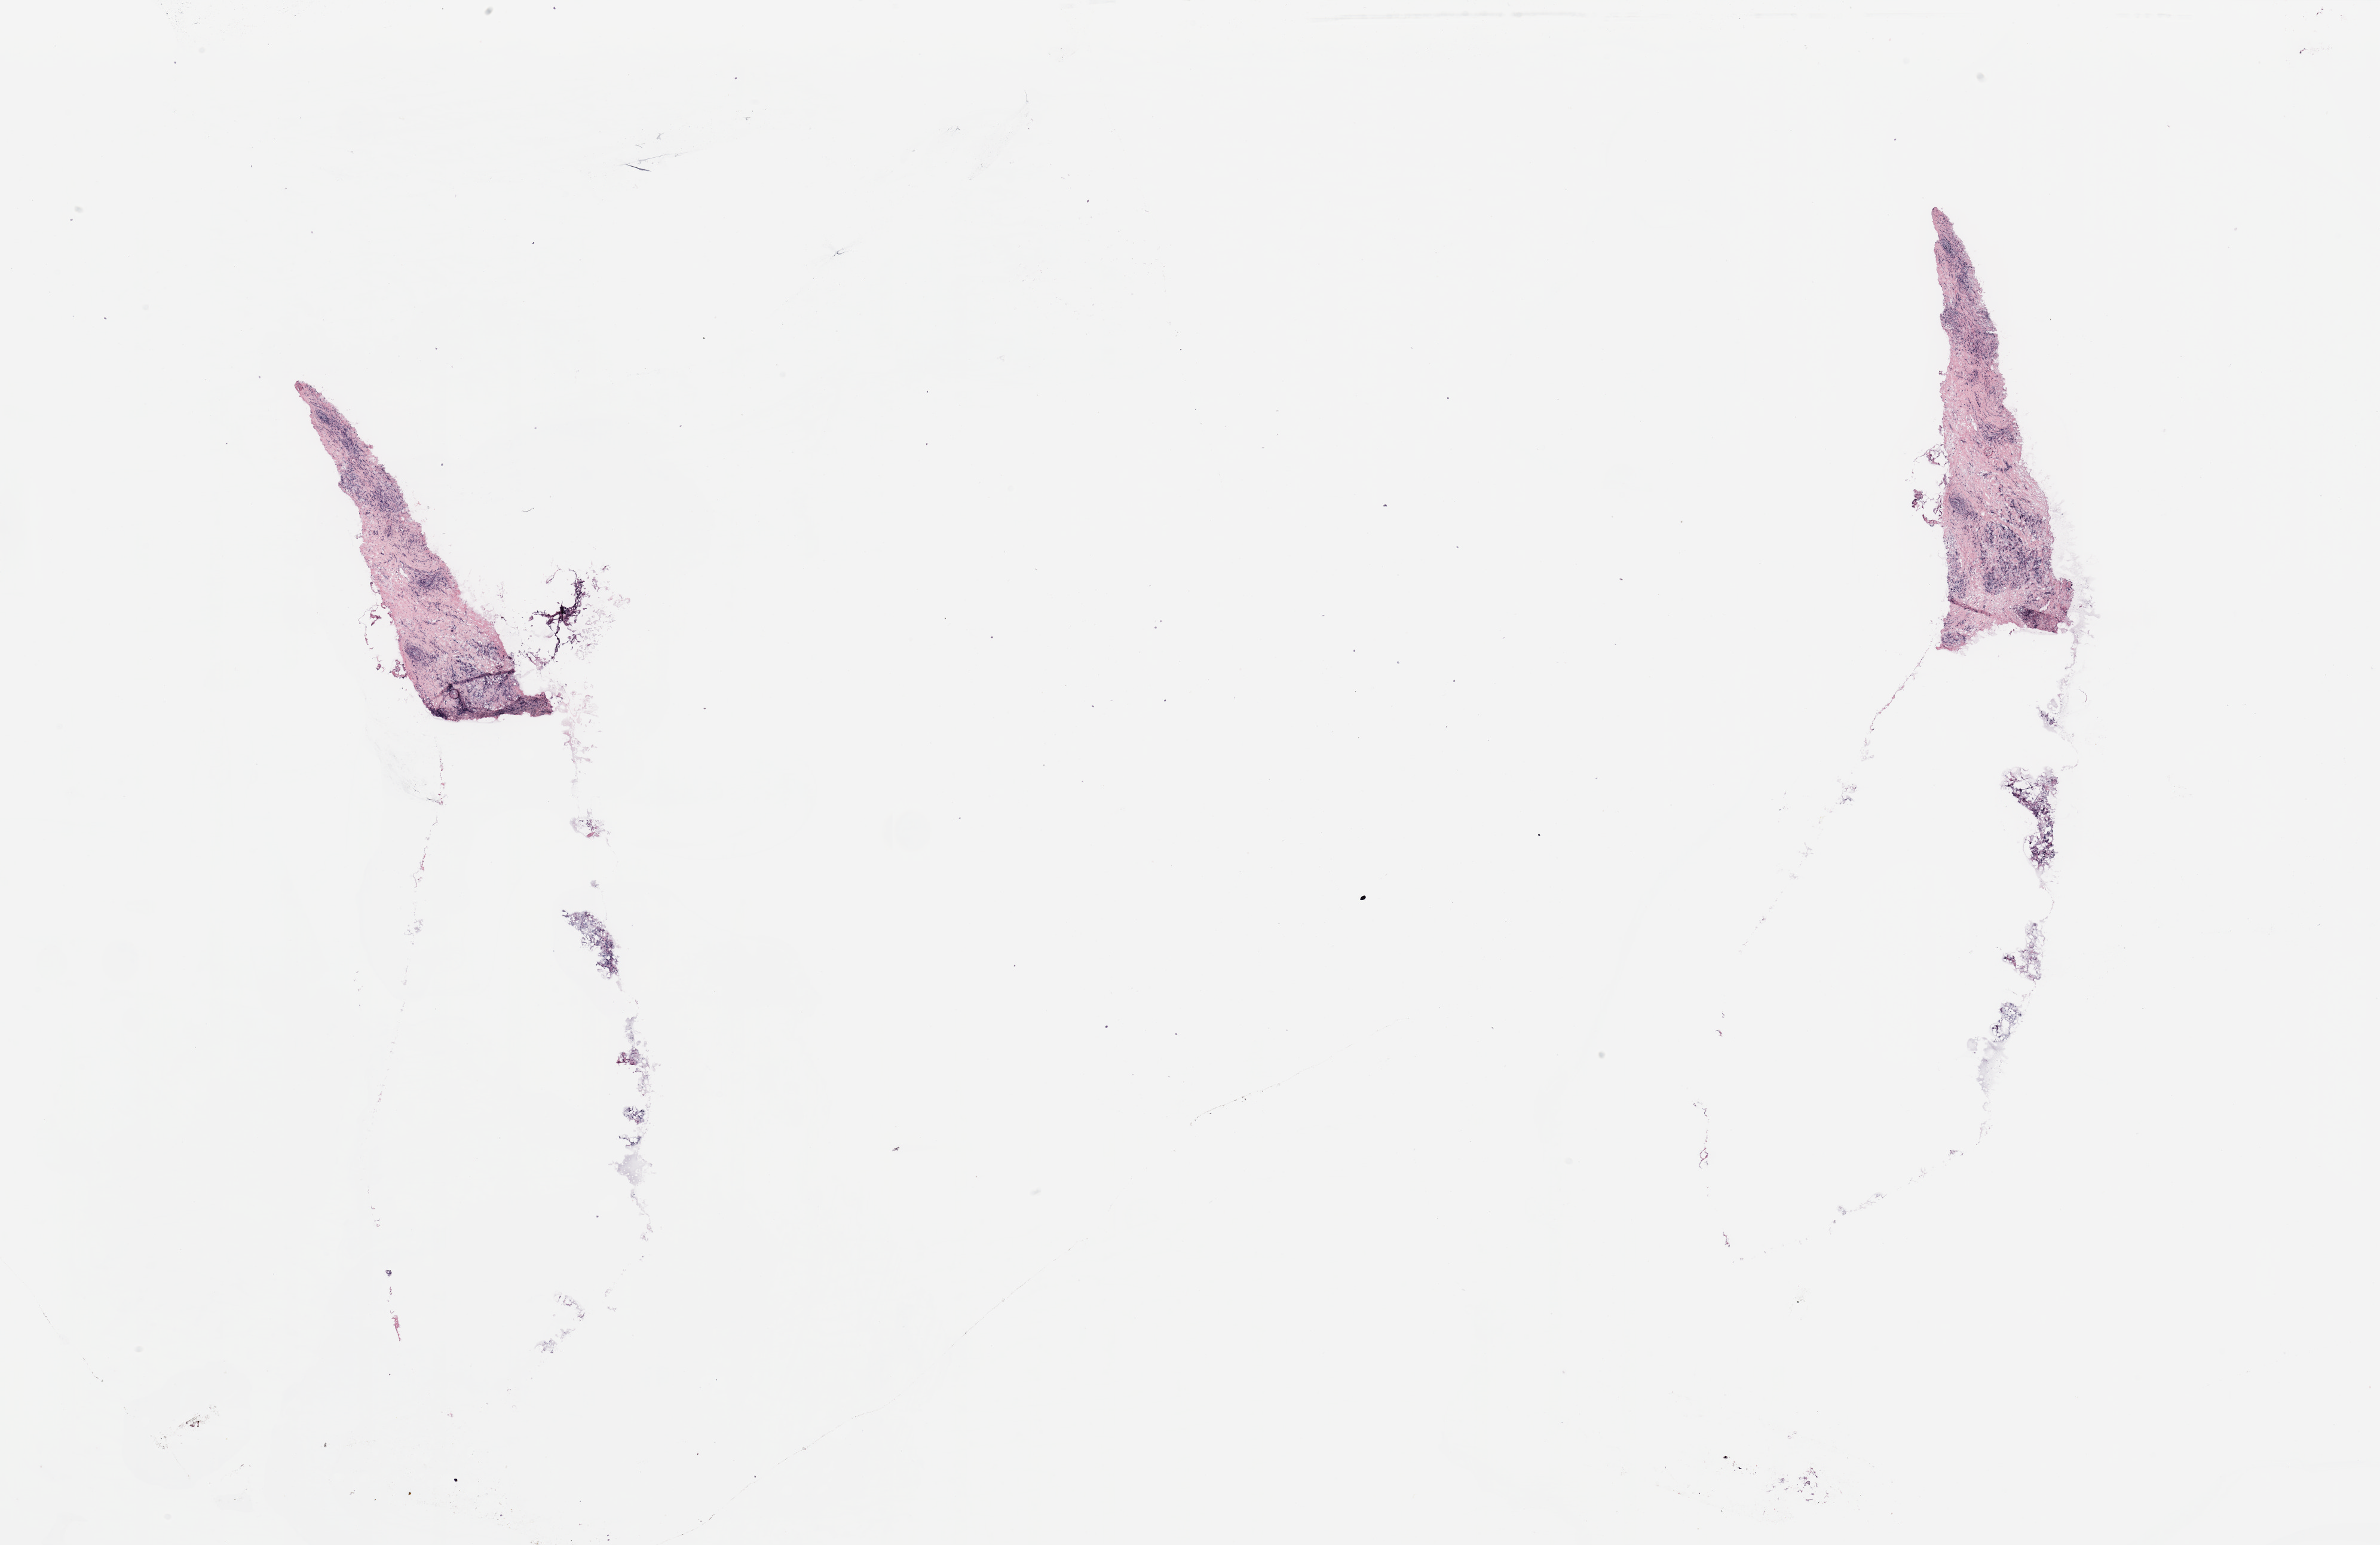
Whole-slide histology image, Hematoxylin and eosin (H&E) stained, shown as a low-resolution overview of the whole scanned area (about 31.5 x 20.4 mm), breast, tissue type not recorded.
Patient diagnosis (cohort enrolment): breast cancer (breast).